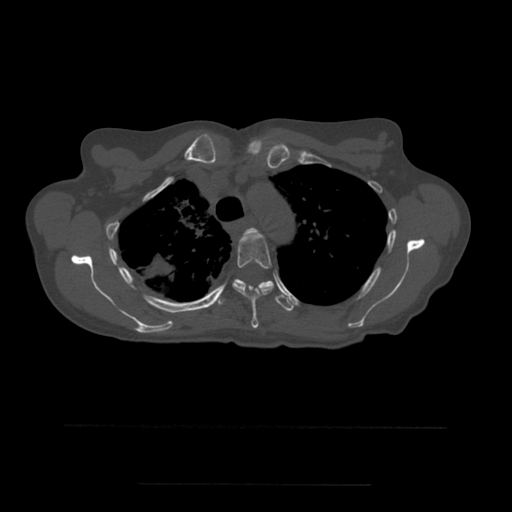
CT including the spine, one axial slice. Slice 404 of 544 in the series (ordered by position). Bone window (W 1800 / L 400 HU). 1.25 mm slice thickness. 512 × 512 image matrix, field of view 350 × 350 mm. Patient age 58 years. Case-level facts recorded for this patient, not image findings: primary cancer: lung.
Annotated regions visible in this slice (semi-automatic segmentation, software-assisted and operator-edited):
- T3 vertebra: bounding box <245,228,260,234> (left, top, right, bottom; pixels)
- T4 vertebra: <233,233,274,329>
- T5 vertebra: <219,279,296,311>